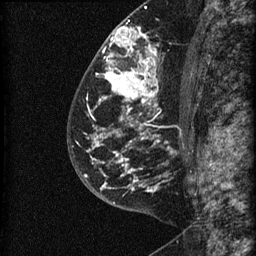
Breast MRI (dynamic contrast-enhanced), one sagittal slice. Slice 39 of 60 in the series (ordered by position). Dynamic contrast-enhanced series, image 2 of 3 at this slice position (ordered by acquisition). 1.5 T. TE 4.2 ms, TR 22.7 ms. 1.5 mm slice thickness. 256 × 256 image matrix, field of view 180 × 180 mm. Female patient, age 48 years. From the clinical record (not read from this slice): setting: breast cancer imaged before/during neoadjuvant chemotherapy; receptor status: triple-negative.
Outlined on this slice (semi-automatically segmented with operator editing):
- analysis volume of interest (the breast-tissue region the enhancement analysis was run in; not a lesion): box from (x=81, y=23) to (x=186, y=202) px
- tumour enhancement mask (voxels above the 90 % enhancement threshold inside the analysis volume of interest): (x=85, y=26)–(x=160, y=191)